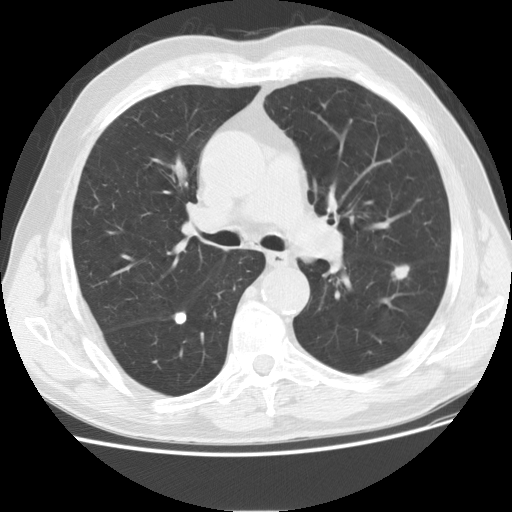
Axial slice from a low-dose chest CT screening exam. Second screening round (one year after baseline). Lung window (W 1500 / L -600 HU). 2.5 mm slice thickness. Standard (soft-tissue) reconstruction kernel (STANDARD). Slice 64 of 175 in the series. Male, age 73 years at enrolment. Current smoker at enrolment.
Lesion marked by an expert reader, bounding box (x1, y1, x2, y2) in pixels: (370, 255, 423, 299). Reader record for this screening exam (exam-level; its link to the box is not recorded): non-calcified nodule or mass ≥4 mm, left lower lobe, 16 × 10 mm, smooth margins, soft tissue attenuation, pre-existing on the prior screen: yes; interval growth: yes. Lung cancer was diagnosed 76 days after this screen: adenocarcinoma, NOS, left lower lobe, poorly differentiated (G3), stage IIA (AJCC 6th edition), 12 mm at pathology.